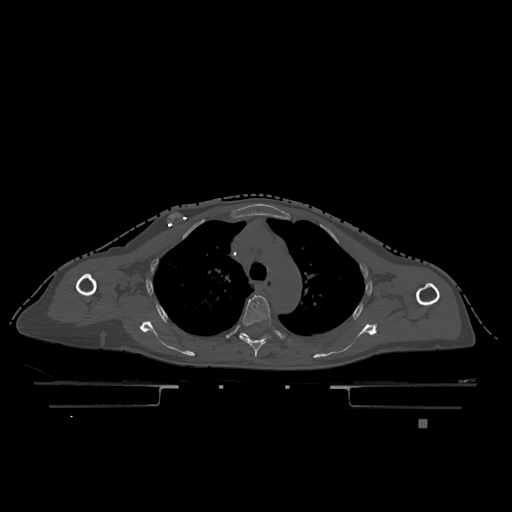
CT including the spine, one axial slice; slice 873 of 1317 in the series (ordered by position); bone window (W 1800 / L 400 HU); 0.5 mm slice thickness; 512 × 512 image matrix, field of view 500 × 500 mm. Female patient, age 74 years. Case-level facts recorded for this patient, not image findings: primary cancer: lung; vertebrae with lytic lesions (as recorded): T1, T4, T5, T6, L4, L5.
Annotated regions visible in this slice (semi-automatically segmented with operator editing):
- T4 vertebra: bounding box <239,295,272,357> (left, top, right, bottom; pixels)
- T5 vertebra: <240,333,248,337>